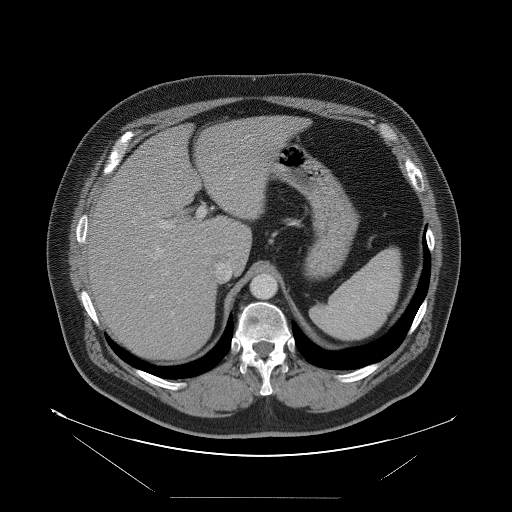
Contrast-enhanced abdominal CT, one axial slice. Slice 68 of 114 in the series (ordered by position). 120 kVp. Intravenous contrast given. Soft-tissue window (W 400 / L 40 HU). 5 mm slice thickness. 512 × 512 image matrix, field of view 500 × 500 mm. Male patient, age 61 years. Case-level facts recorded for this patient, not image findings: diagnosis: colorectal cancer liver metastases, imaged before liver resection; multiple liver metastases: no; largest metastasis: 6.5 cm; chemotherapy before resection: no.
Annotated regions visible in this slice (outlined manually by an expert reader):
- hepatic veins: bounding box (x1, y1, x2, y2) in pixels: (153, 176, 234, 282)
- liver: (88, 116, 299, 359)
- planned liver remnant (the part of the liver to remain after resection): (144, 116, 299, 272)
- portal vein (with intrahepatic branches): (141, 207, 206, 302)